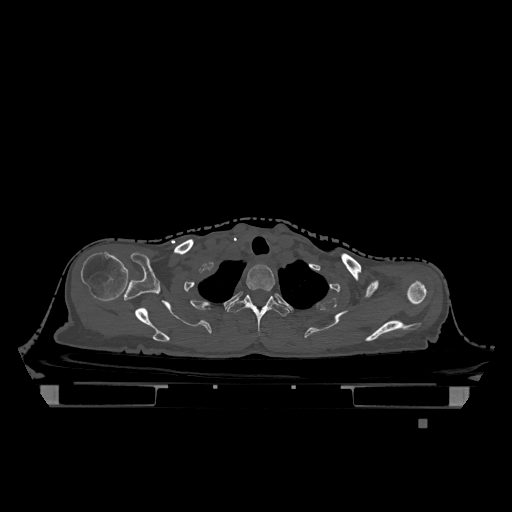
CT including the spine, one axial slice. Slice 977 of 1317 in the series (ordered by position). Bone window (W 1800 / L 400 HU). 0.5 mm slice thickness. 512 × 512 image matrix, field of view 500 × 500 mm. Patient: female, 74 years. From the clinical record (not read from this slice): primary cancer: lung; vertebrae with lytic lesions (as recorded): T1, T4, T5, T6, L4, L5.
Structures marked on this image (semi-automatically segmented with operator editing):
- T1 vertebra: bounding box [x1, y1, x2, y2] px = [246, 265, 275, 291]
- T2 vertebra: [227, 295, 290, 331]